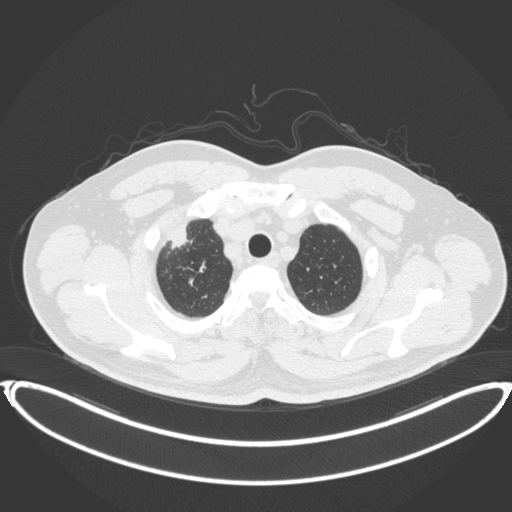
Chest CT, one axial slice; reconstruction kernel B31f; 120 kVp; lung window (W 1500 / L -600 HU); 512 × 512 image matrix, field of view 445 × 445 mm. Patient: male, 53 years. From the clinical record (not read from this slice): clinical TNM (as recorded): T2a N0 M0.
Outlined on this slice (bounding box drawn by a radiologist):
- lung tumour (recorded histology: adenocarcinoma): box from (x=163, y=224) to (x=199, y=255) px